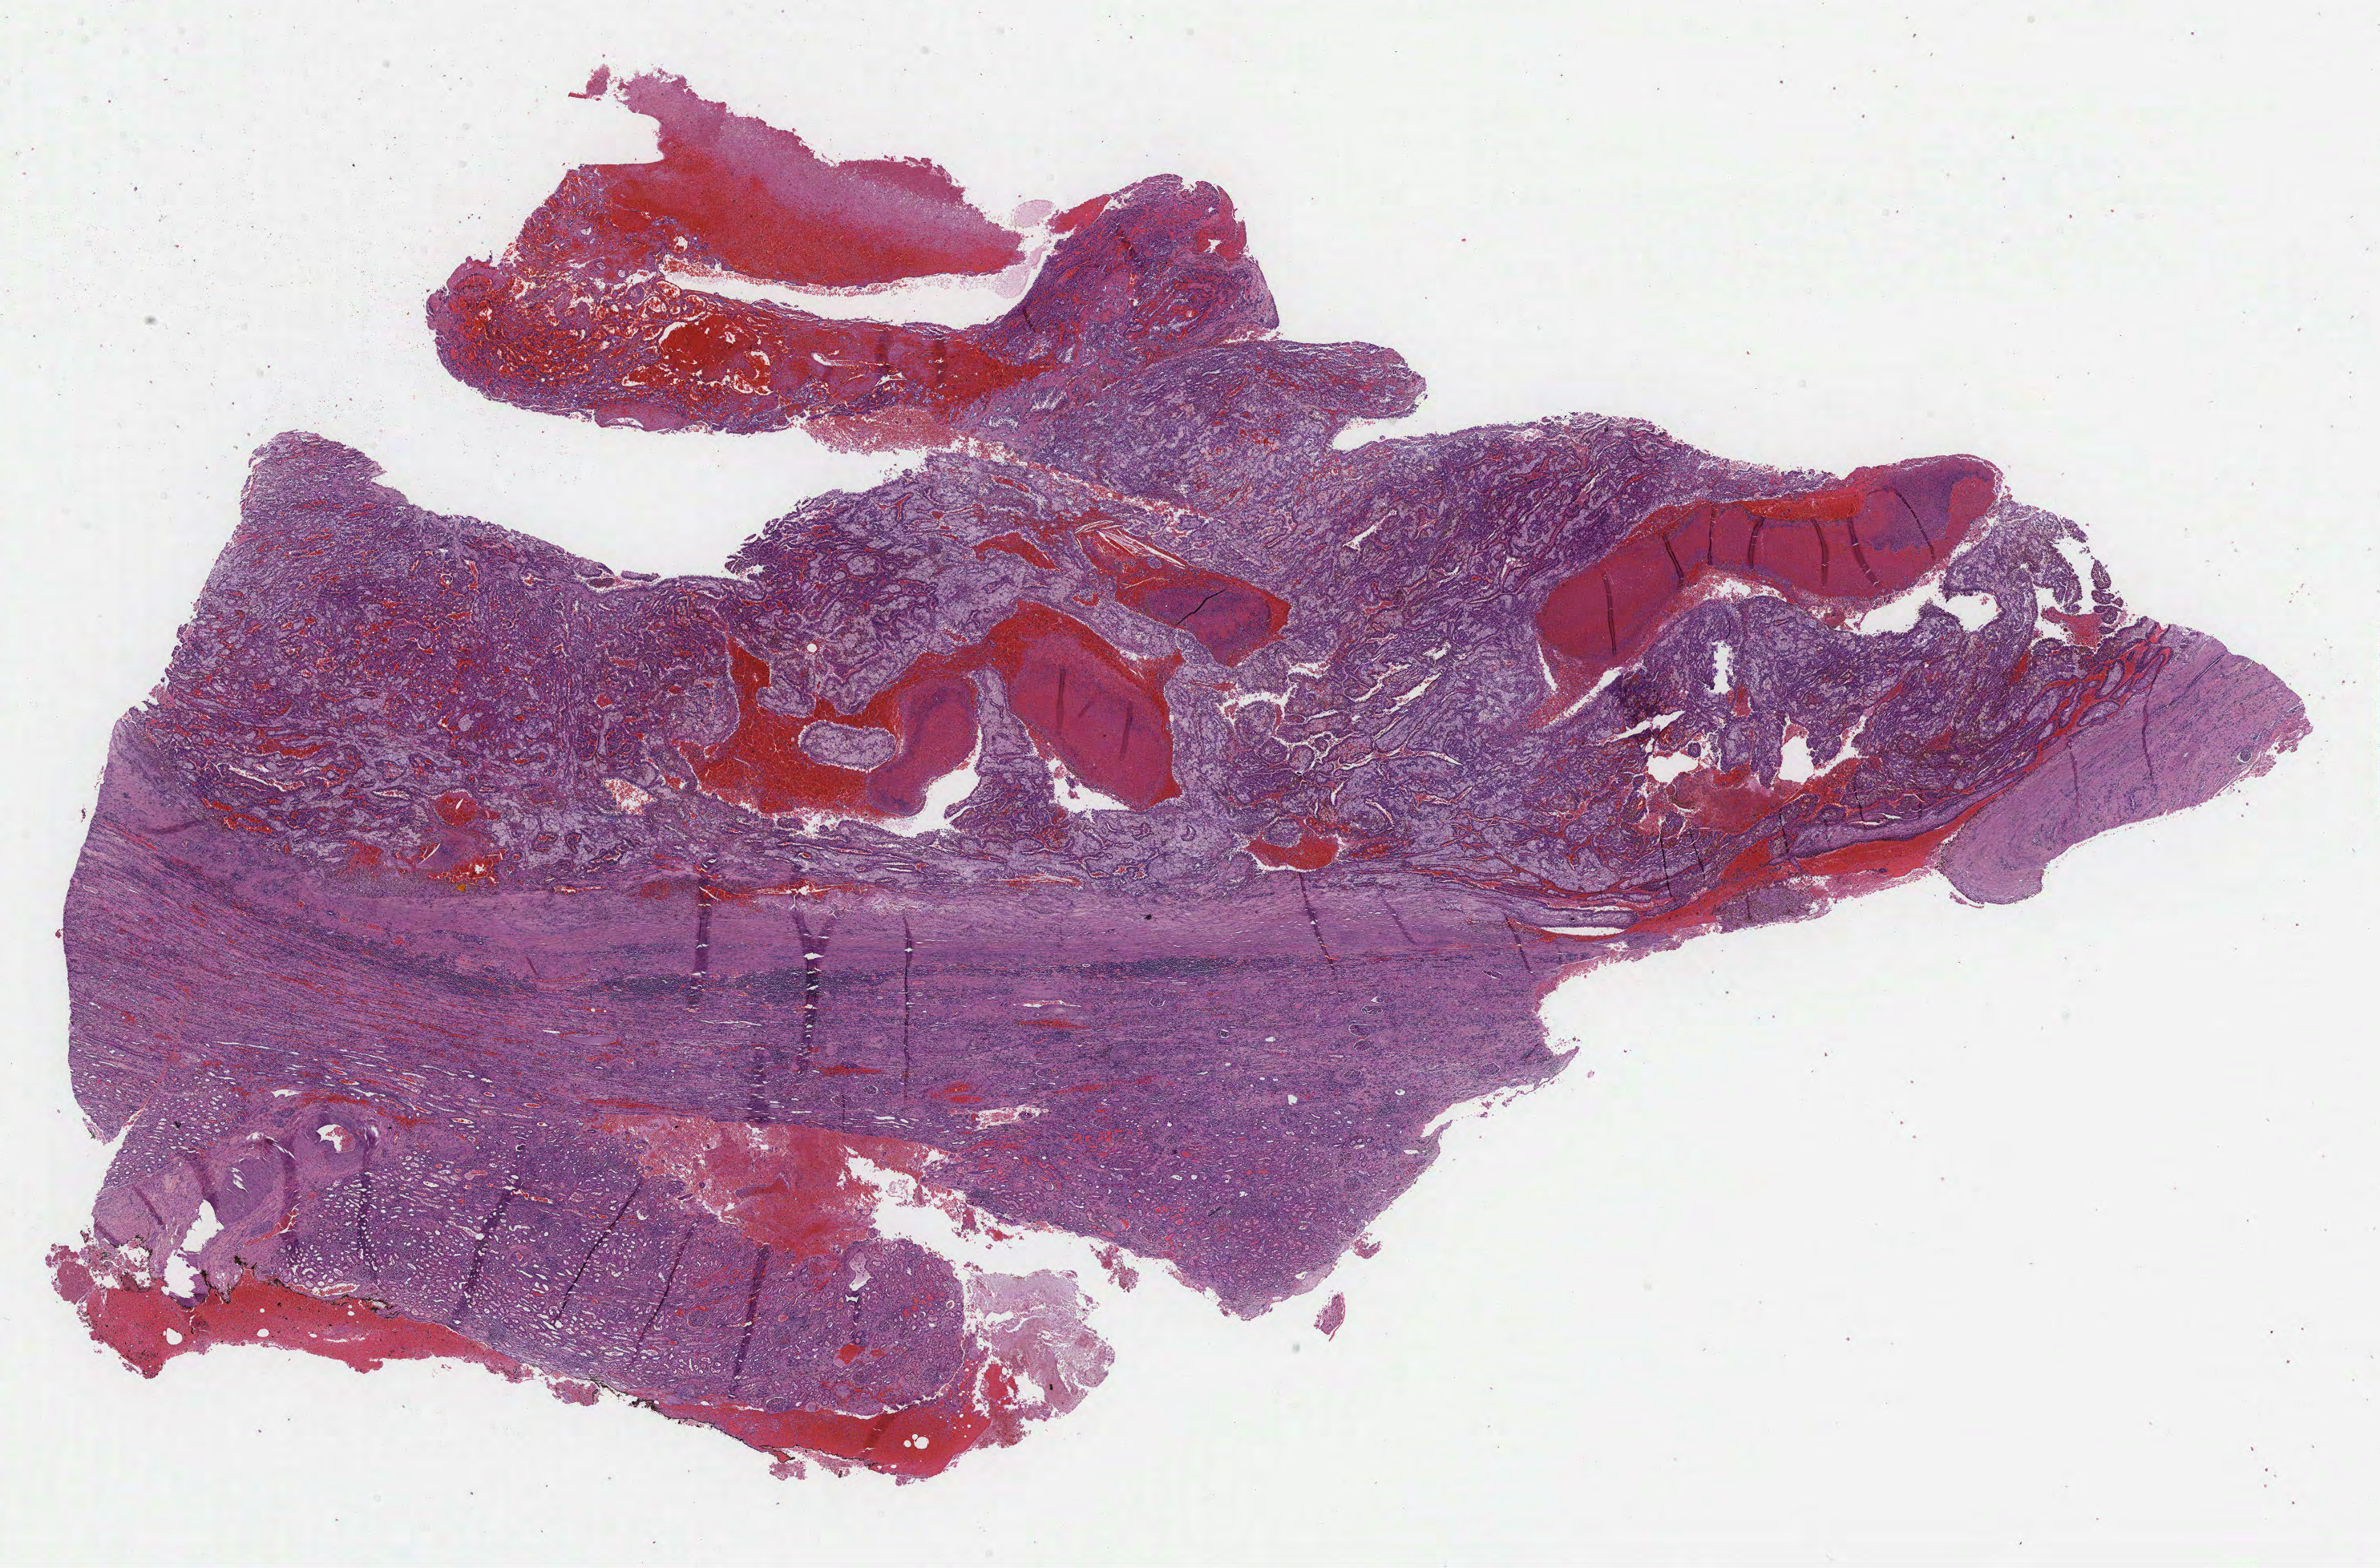
Digitized Hematoxylin and eosin (H&E) stained tissue section (whole slide) — shown as a low-resolution overview of the whole scanned area (about 24.0 x 15.8 mm, slide scanned at 40x), formalin-fixed paraffin-embedded (FFPE) diagnostic section, sample: primary tumour, kidney. Male, age 80 years at initial diagnosis.
AJCC pathologic stage: II. Diagnosis: Papillary adenocarcinoma, NOS.